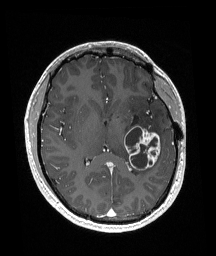
Brain MRI from a brain-tumour surgery series, one axial slice; slice 90 of 192 in the series (ordered by position); T1-weighted post-contrast; 1 mm slice thickness; 216 × 256 image matrix, field of view 211 × 250 mm. From the clinical record (not read from this slice): histopathology: Glioneuronal tumor; WHO grade: 2.
Outlined on this slice (expert manual segmentation):
- tumour: bounding box (x1, y1, x2, y2) in pixels: (124, 125, 161, 171)